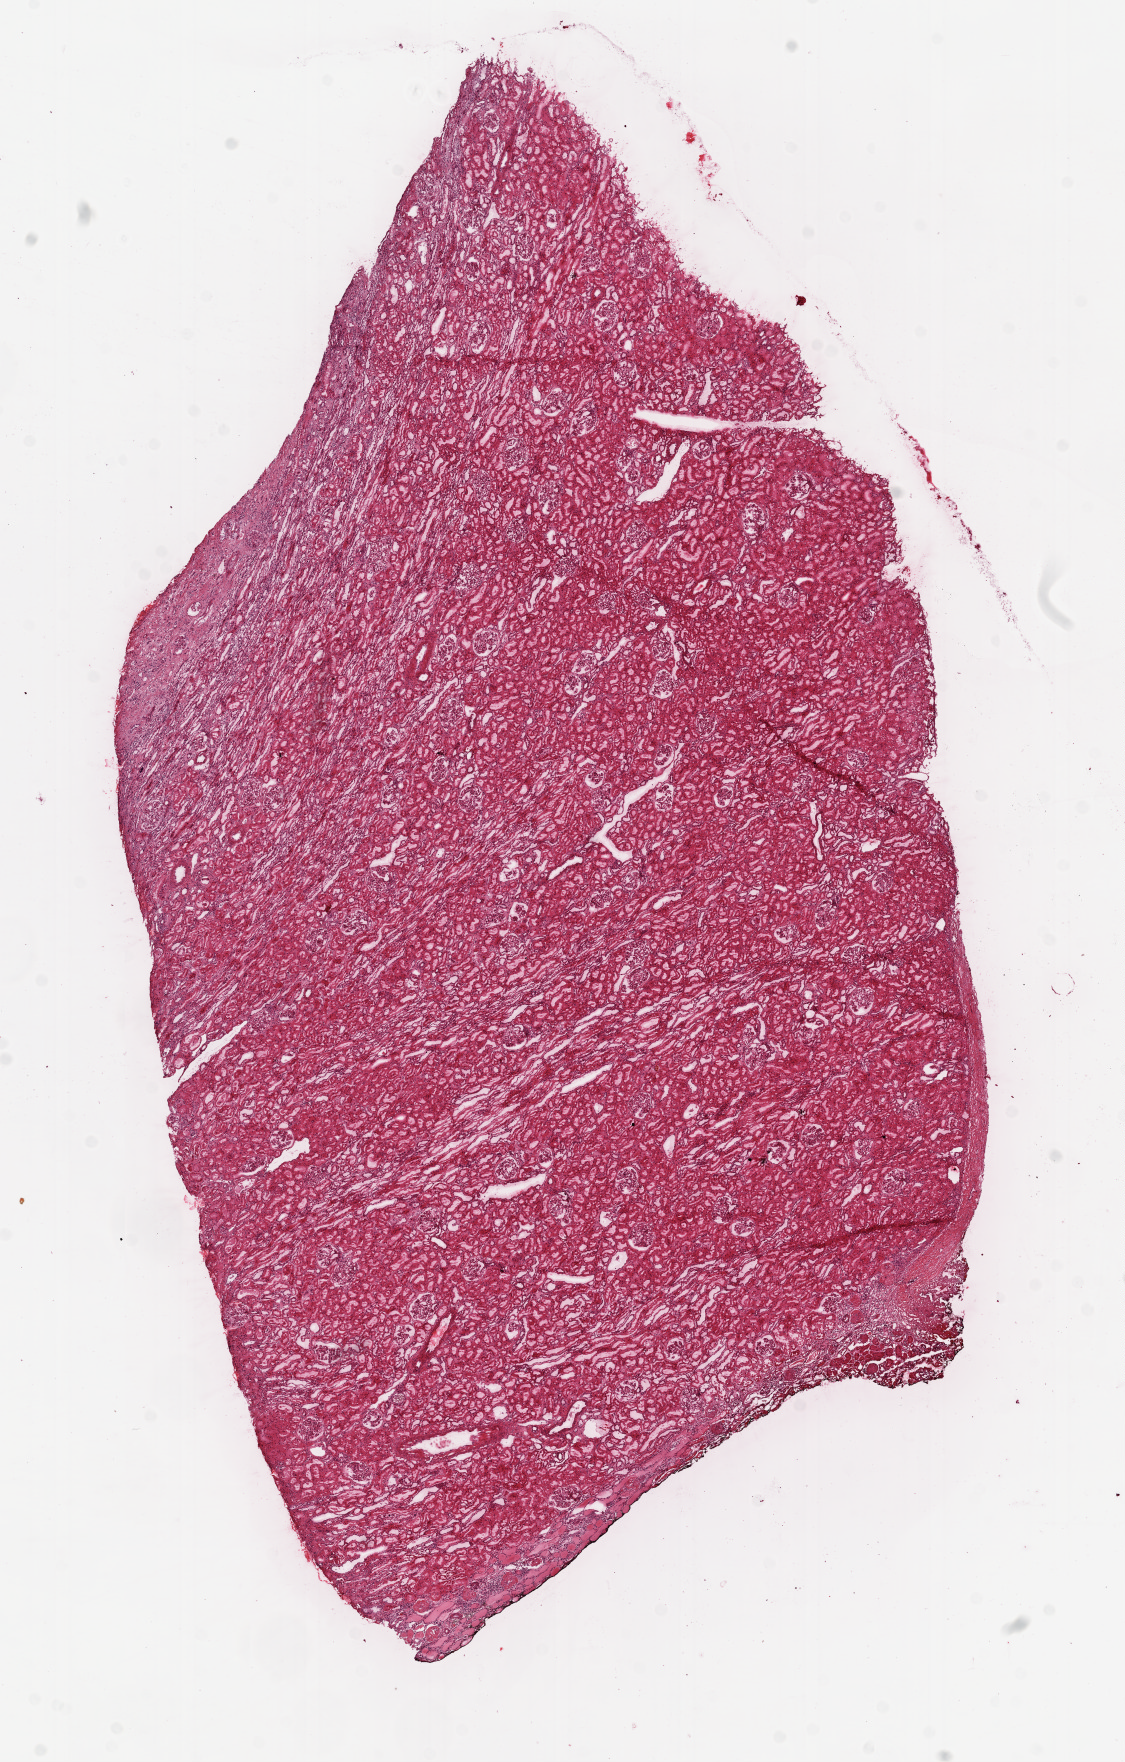
Digitized Hematoxylin and eosin (H&E) stained tissue section (whole slide), low-resolution overview of the scanned area, about 9.0 x 14.1 mm (from a 20x scan). Frozen section from the top of the tissue portion. Solid tissue normal (non-tumour tissue) sample from the kidney. Female patient; age at initial diagnosis 41 years.
This section: solid tissue normal sample (biorepository sample class). Patient diagnosis: Clear cell adenocarcinoma, NOS.